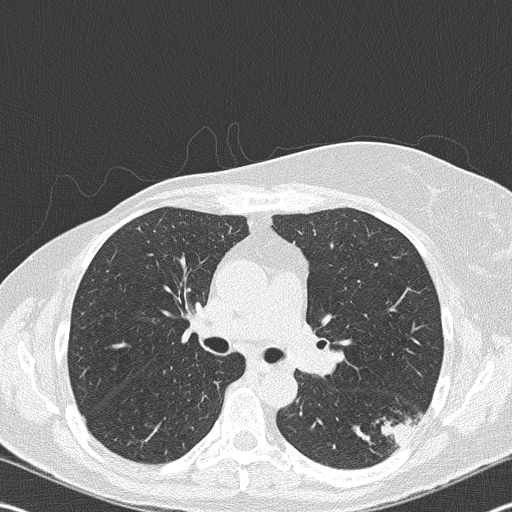
Chest CT (low-dose screening protocol), one axial image. Second annual screen. Lung window (W 1500 / L -600 HU). 120 kVp. Female, age 60 years at enrolment. Current smoker at enrolment.
Expert-annotated lung lesion, bounding box <366,388,431,450> (left, top, right, bottom; pixels). Screening reader's record for this exam (one nodule recorded; not confirmed to be the boxed lesion): non-calcified nodule or mass ≥4 mm, left lower lobe, 18 × 16 mm, spiculated (stellate) margins, soft tissue attenuation, pre-existing on the prior screen: no. Later outcome: lung cancer diagnosed 35 days after this screen — carcinoma, NOS, left hilum, stage IV (AJCC 6th edition), 45 mm at pathology.